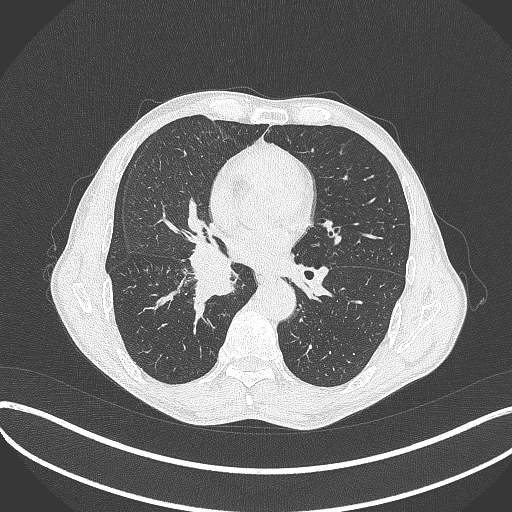
Chest CT, one axial slice. Slice 210 of 481 in the series (ordered by position). Reconstruction kernel B70f. 120 kVp. Lung window (W 1500 / L -600 HU). 1 mm slice thickness. 512 × 512 image matrix, field of view 400 × 400 mm. Patient: male, 65 years. Case-level facts recorded for this patient, not image findings: clinical TNM (as recorded): T2a N0 M0; histopathological grade: G2.
Outlined on this slice (rectangle marked by the reading radiologist):
- lung tumour (recorded histology: squamous cell carcinoma): box from (x=182, y=240) to (x=248, y=303) px